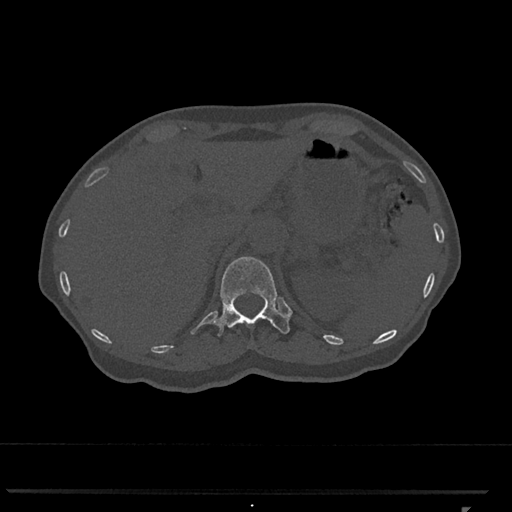
CT including the spine, one axial slice. Position 465 of 793 along the scan axis. Bone window (W 1800 / L 400 HU). 512 × 512 image matrix. Female patient, age 62 years. Case-level facts recorded for this patient, not image findings: primary cancer: renal.
Structures marked on this image (semi-automatic segmentation, software-assisted and operator-edited):
- T12 vertebra: box from (x=211, y=256) to (x=290, y=336) px